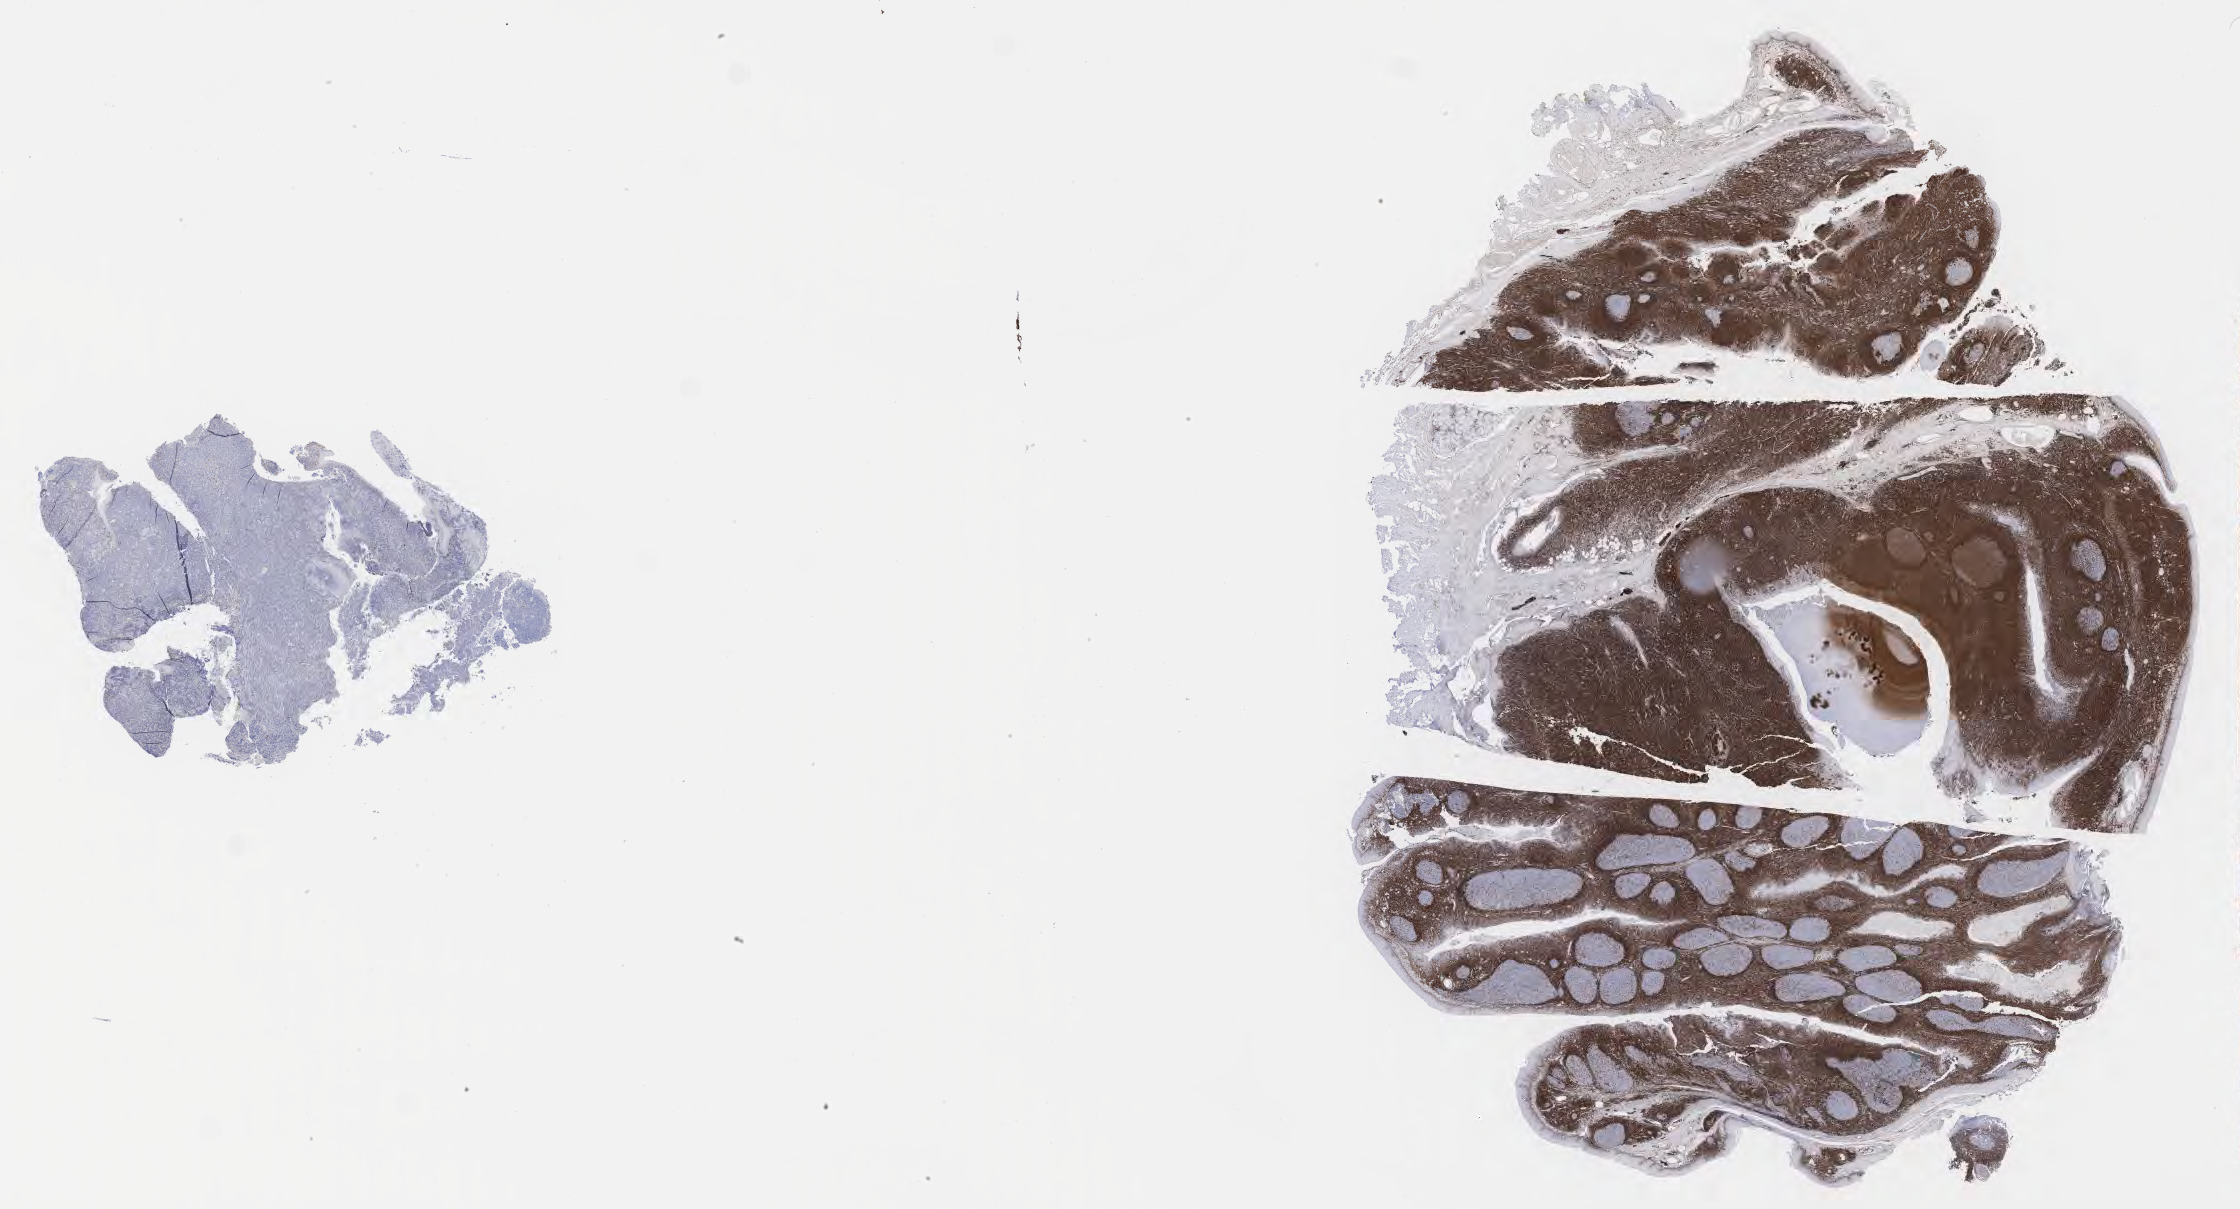
Immunohistochemistry (IHC) whole-slide image stained for BCL2 — a low-resolution overview of the entire scanned area, about 36.2 x 19.6 mm; specimen: tumor tissue. Male, age 3 years at initial diagnosis.
* diagnosis: Burkitt lymphoma, NOS